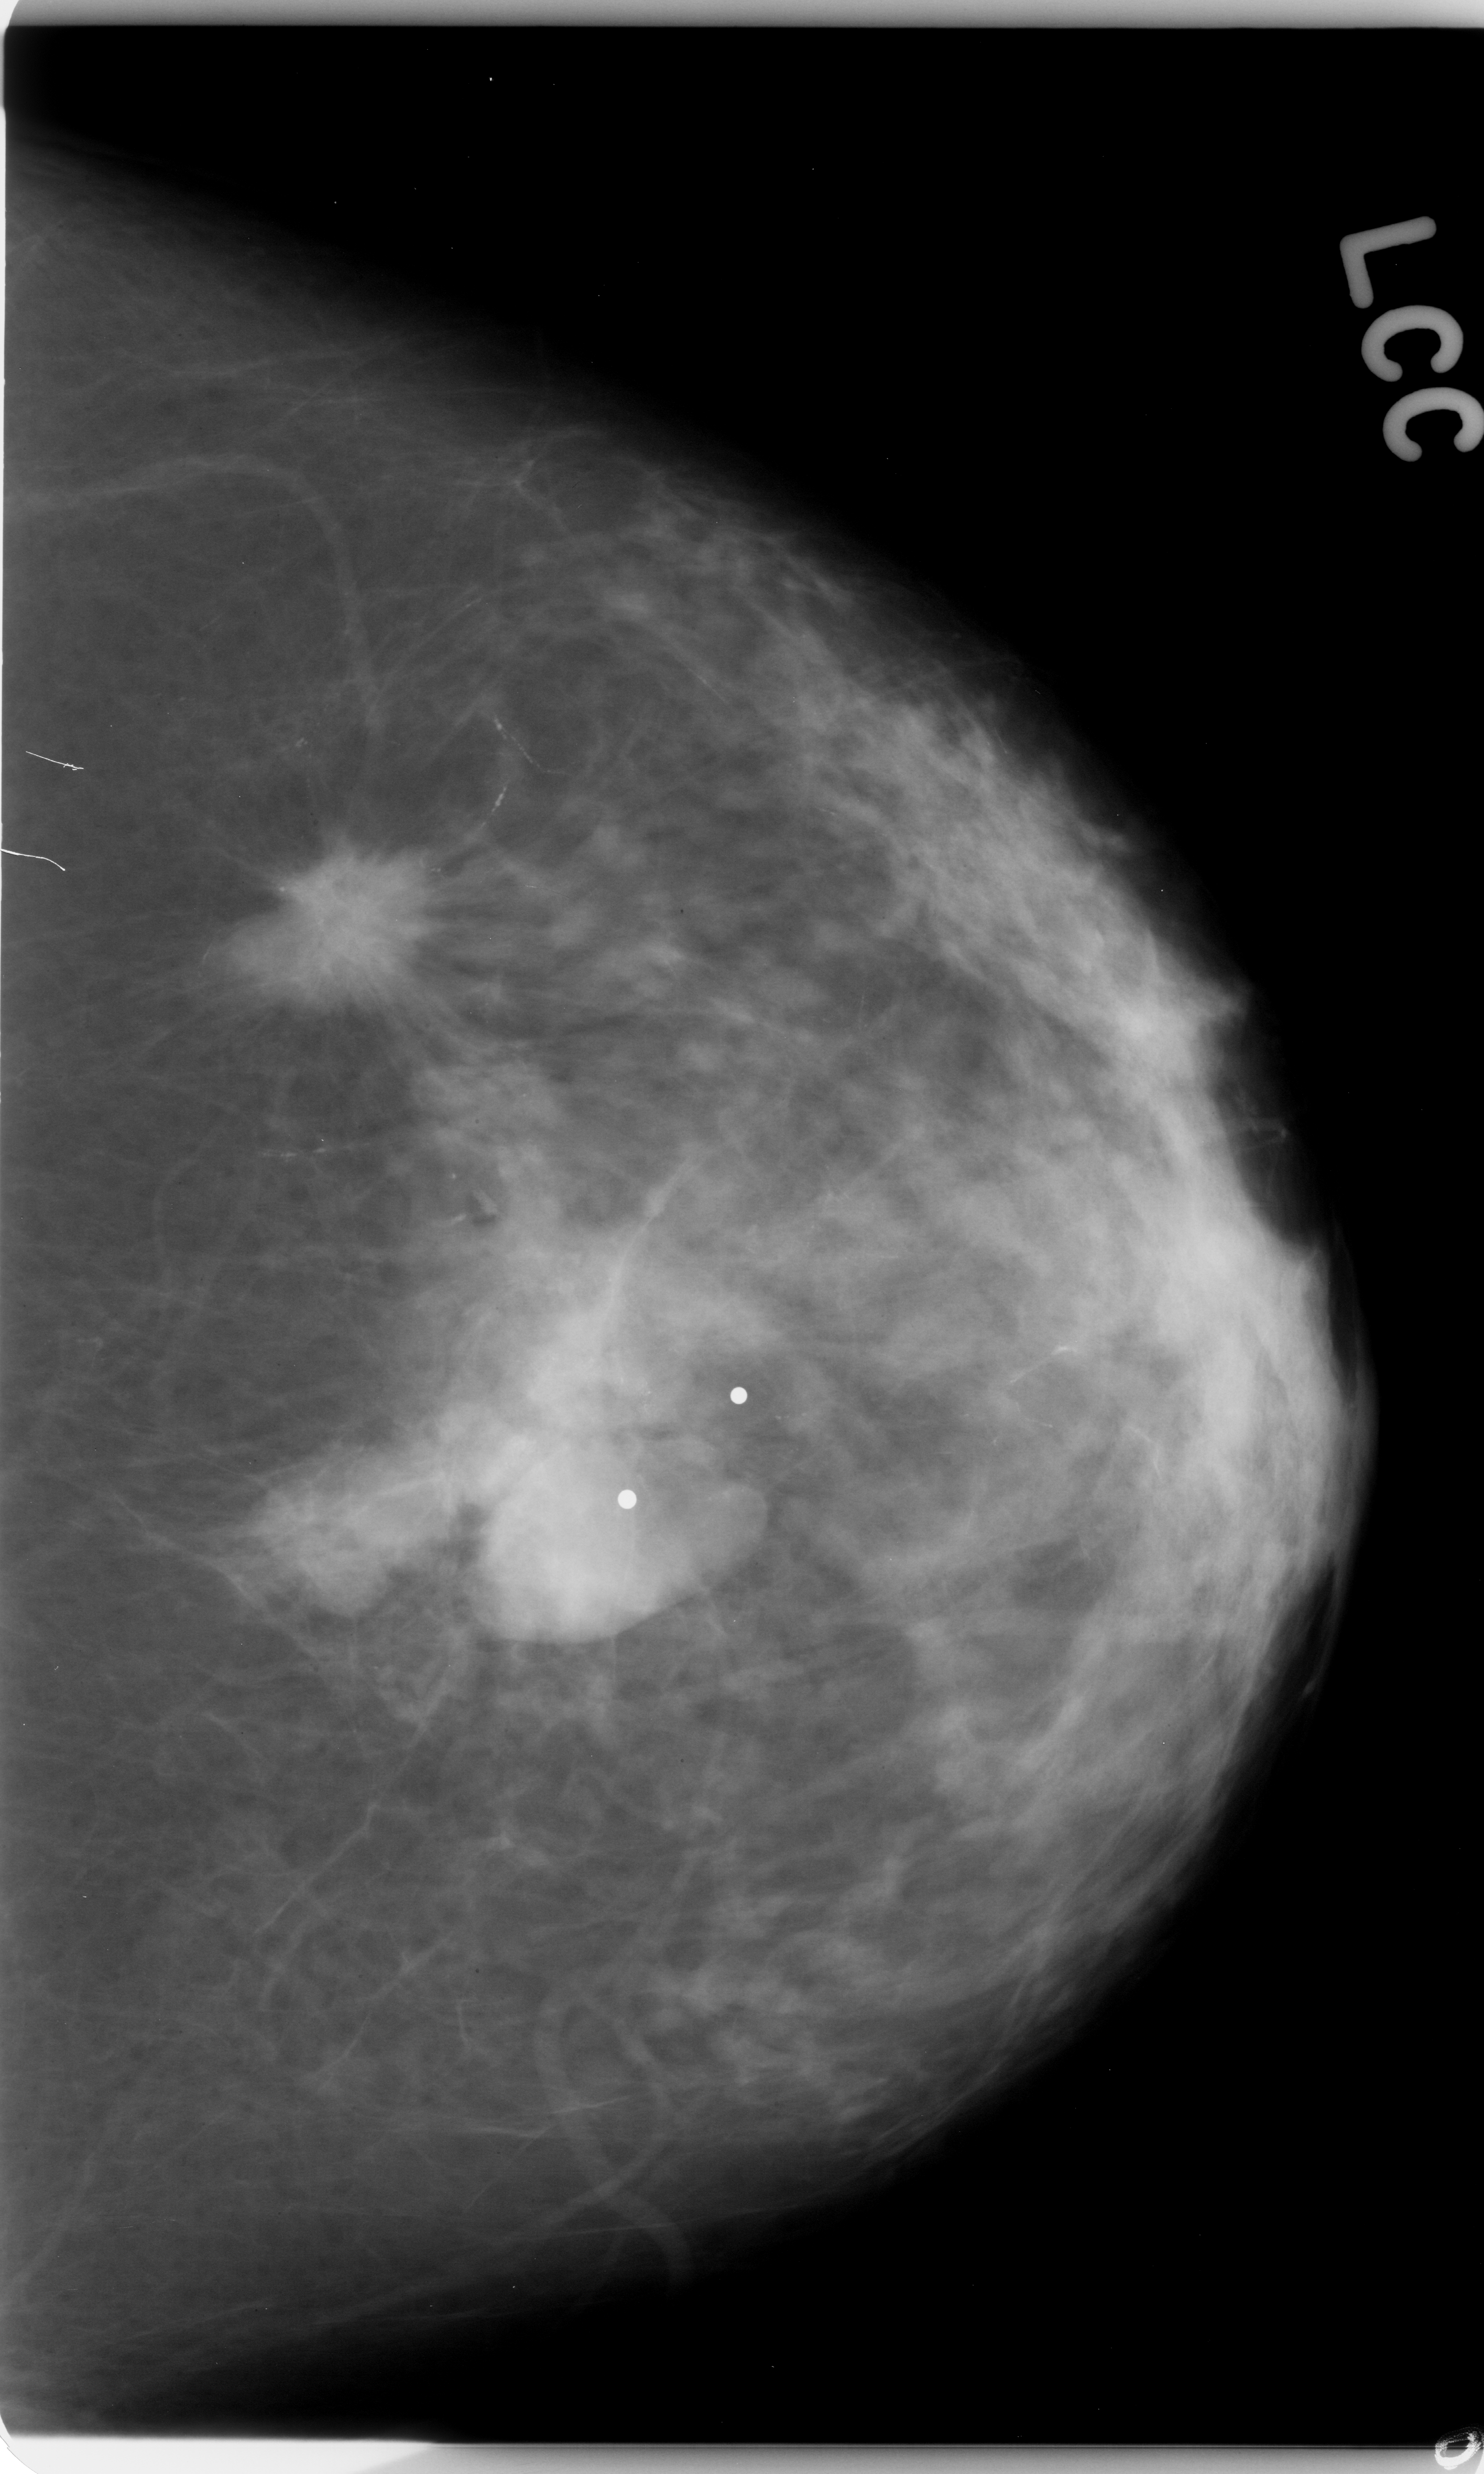
Mammogram (digitized film); left breast; craniocaudal (CC) view; 1484 × 2474 image matrix.
Expert-marked regions of interest on this image (one box per marked abnormality):
- mass, shape irregular, margins spiculated; BI-RADS assessment category 5; pathology (as recorded): malignant: bounding box [x1, y1, x2, y2] px = [298, 1136, 793, 1692]